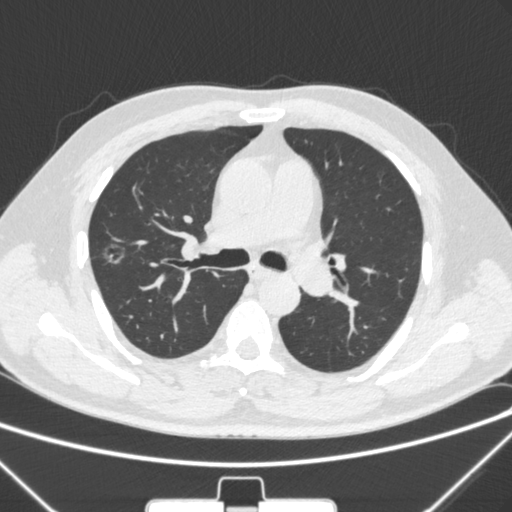
Chest CT, one axial slice. Slice 194 of 320 in the series (ordered by position). Lung window (W 1500 / L -600 HU). 1 mm slice thickness. 512 × 512 image matrix. Patient: male, 58 years. From the clinical record (not read from this slice): clinical TNM (as recorded): T1c N0 M0.
Annotated regions visible in this slice (rectangle marked by the reading radiologist):
- lung tumour (recorded histology: adenocarcinoma): bounding box (x1, y1, x2, y2) in pixels: (99, 238, 131, 268)